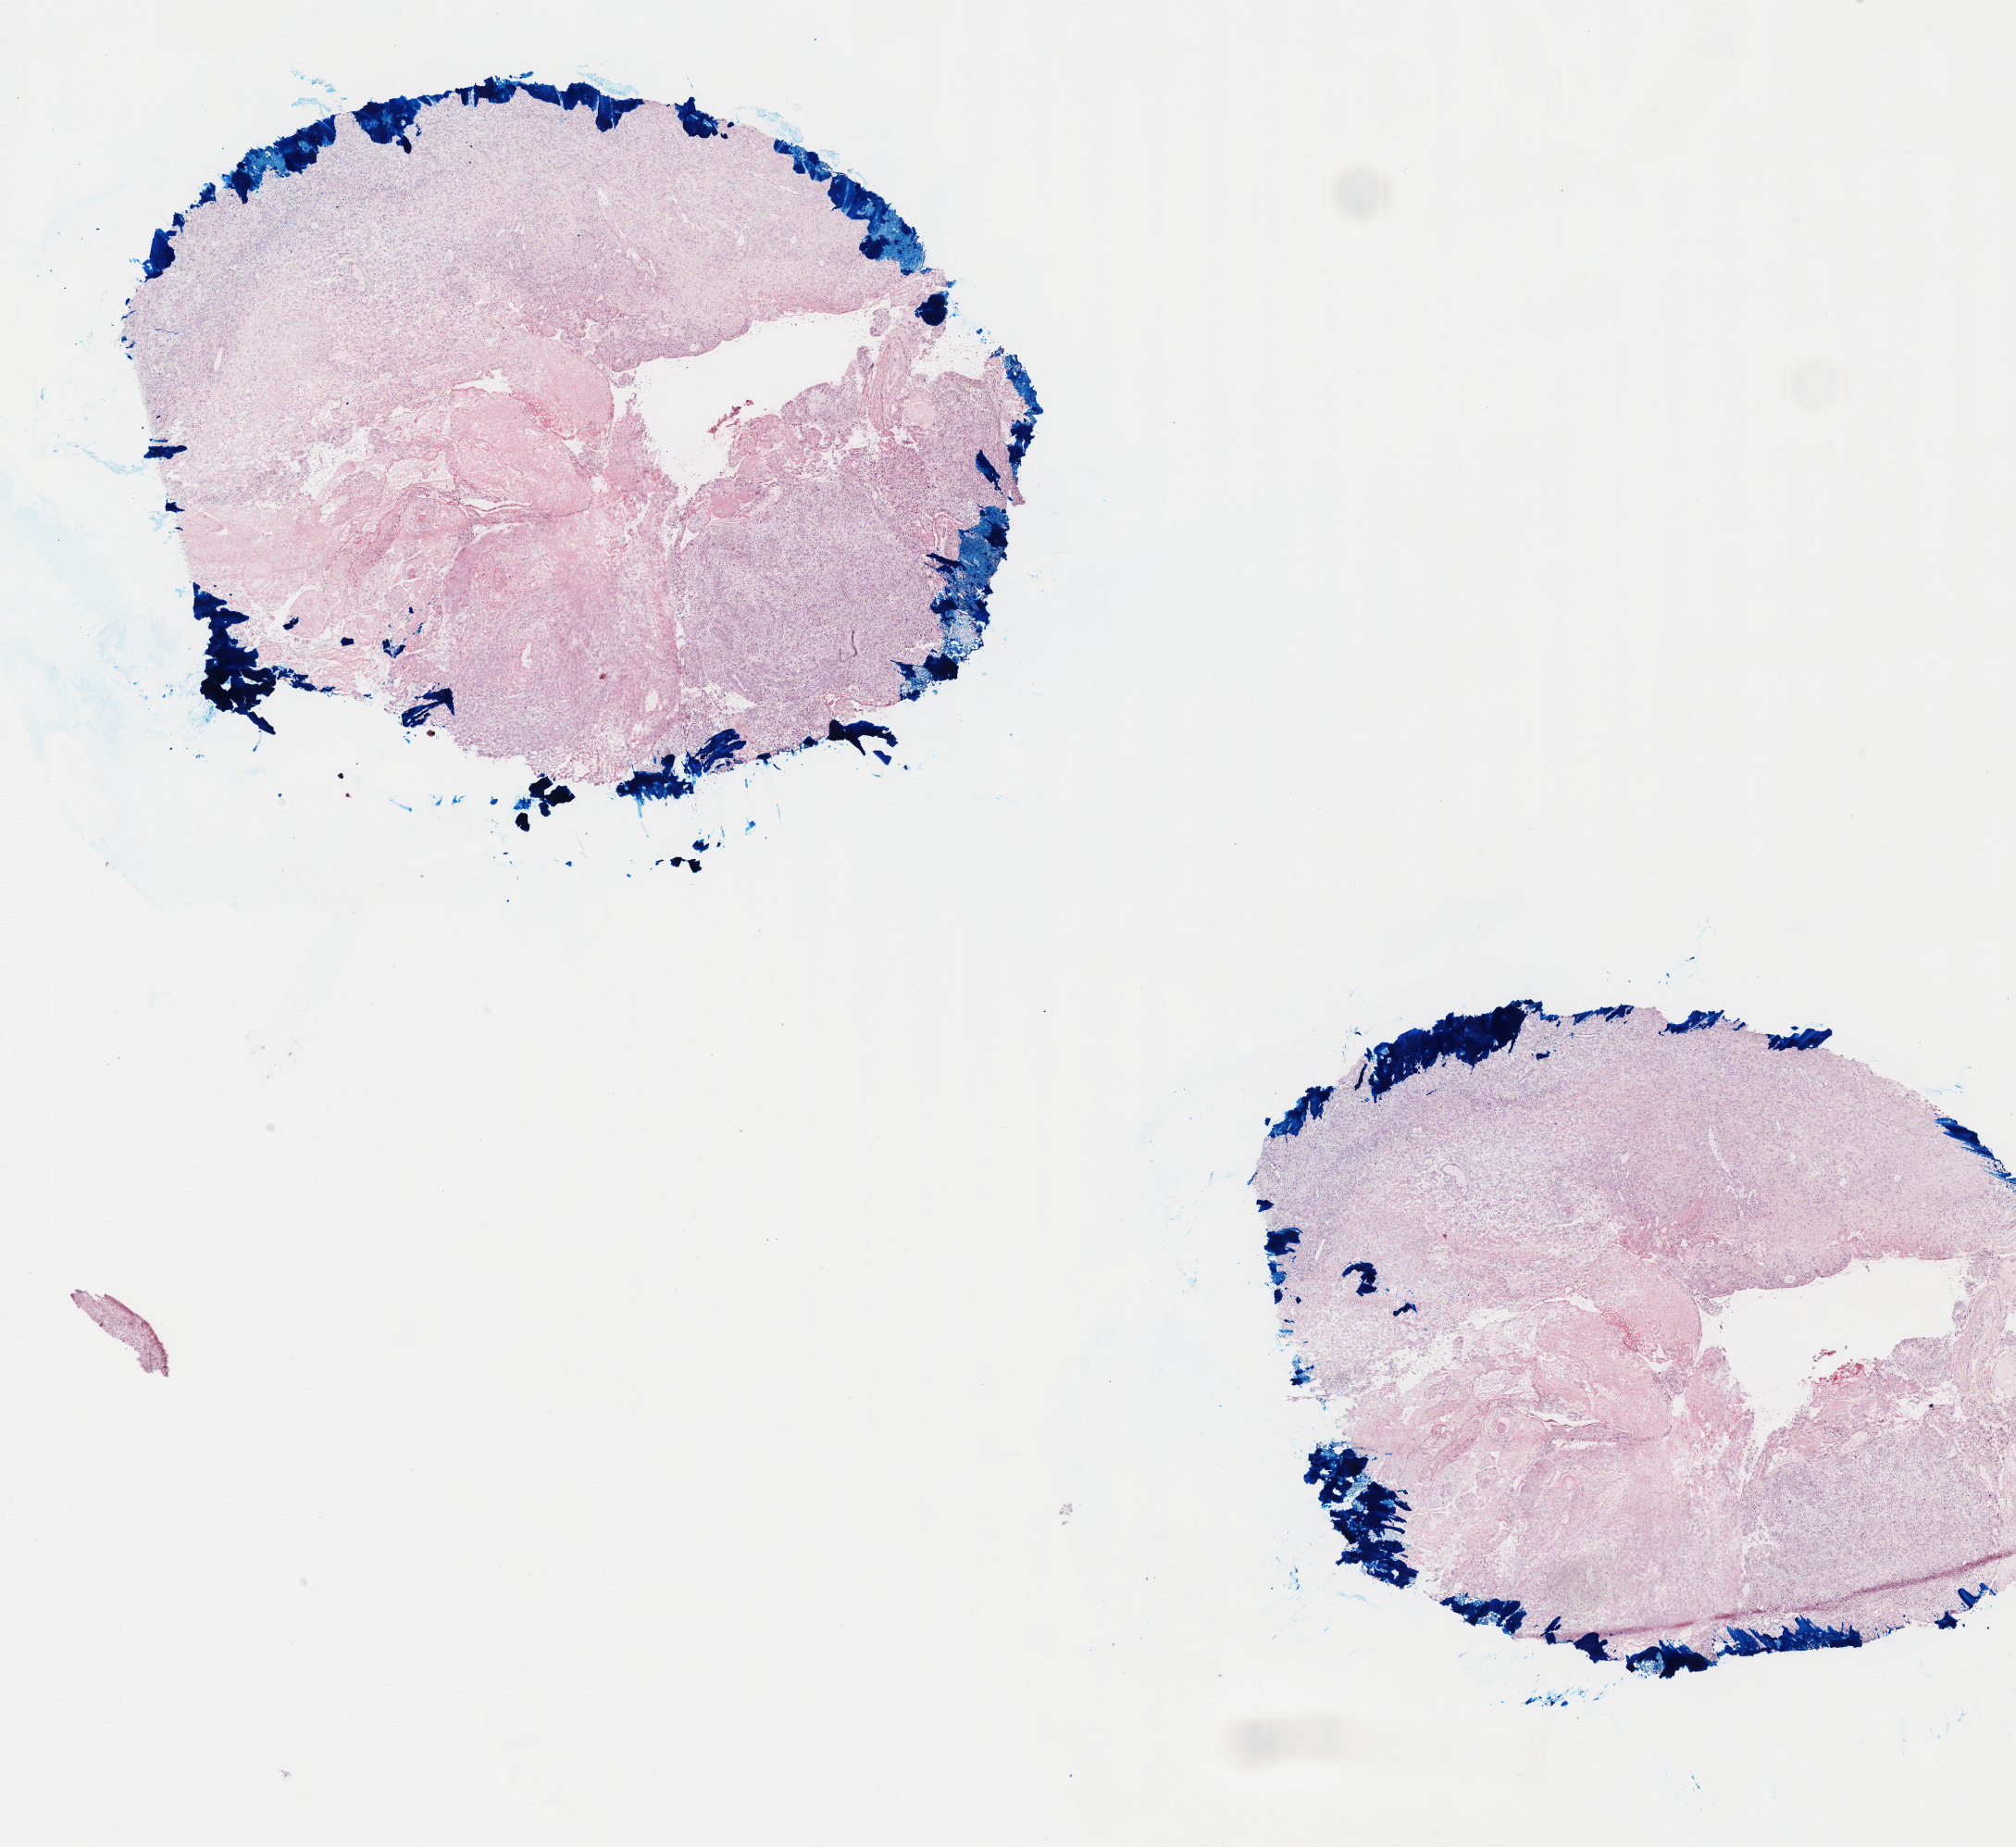
Digitized H&E tissue section (whole slide), a low-resolution overview of the entire scanned area, about 17.6 x 16.1 mm (from a 40x scan). Frozen section from the top of the tissue portion. Brain, primary tumour sample. Male, age 62 years at initial diagnosis. Pathologist review of this section (percent, as recorded): tumour cells 60%, tumour nuclei 100%, normal cells 0%, stromal cells 0%, necrosis 40%.
- histologic diagnosis: Glioblastoma